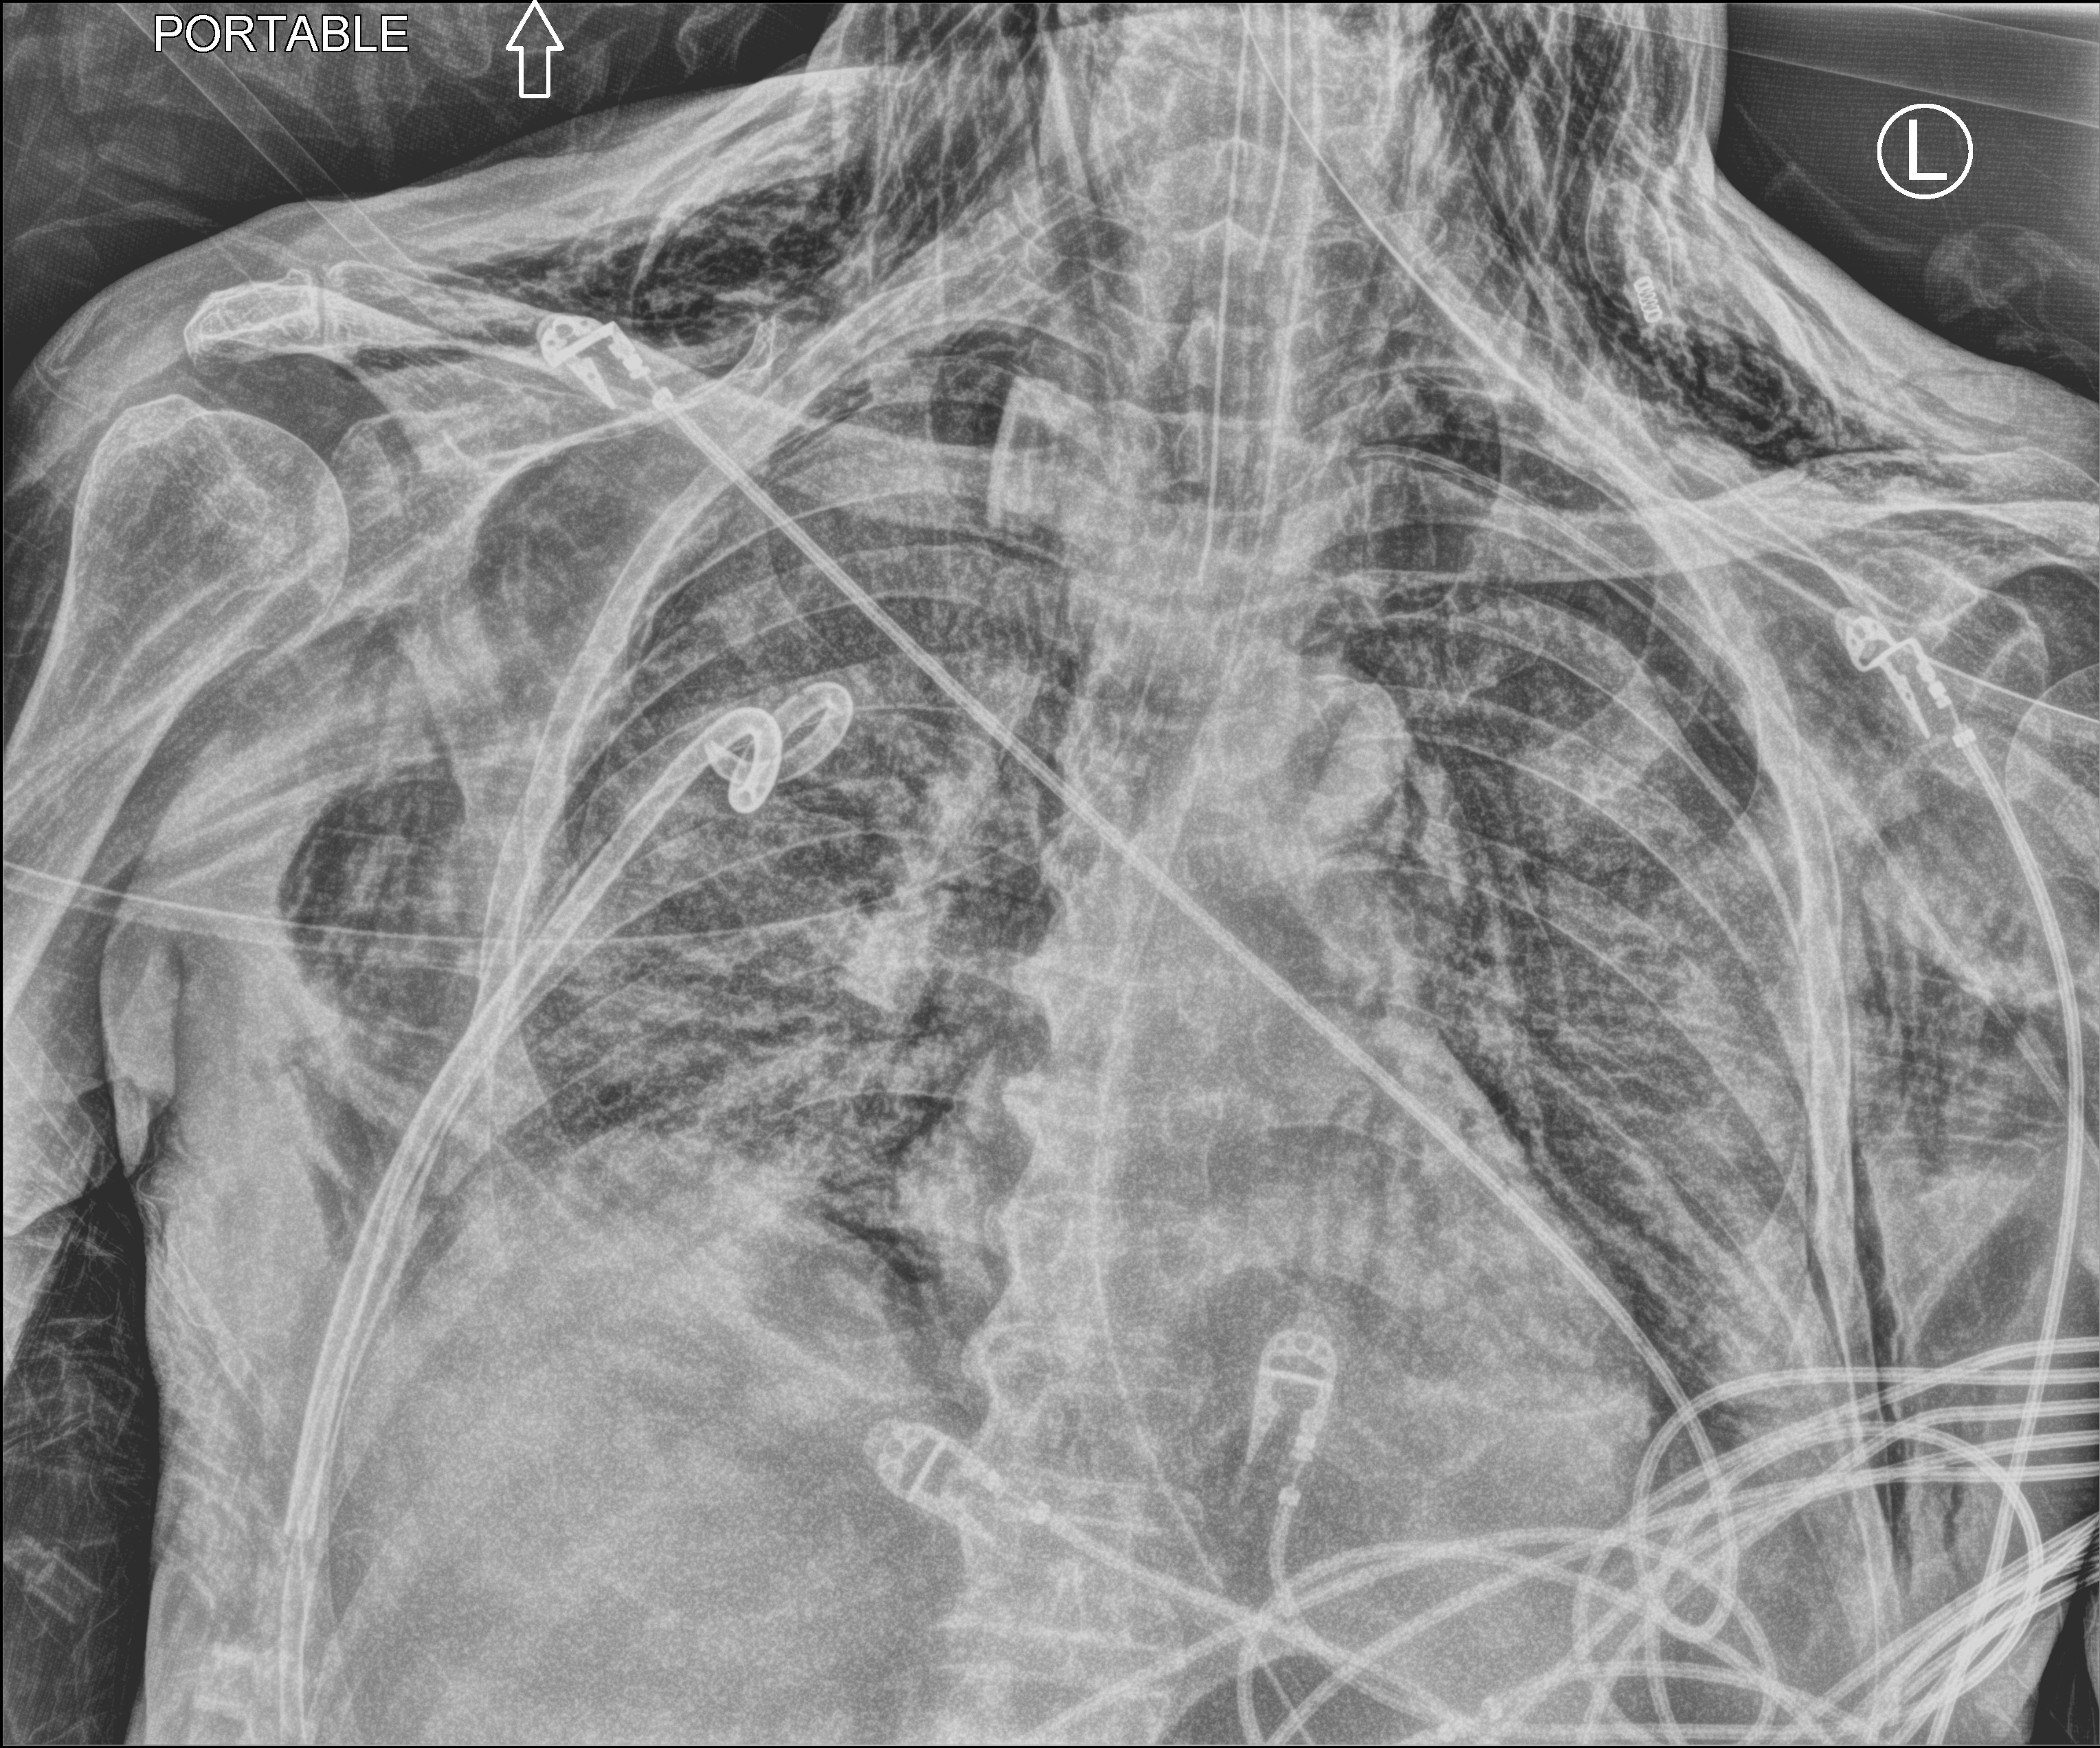
Chest X-ray (portable); anteroposterior (AP) projection. Male patient hospitalised with COVID-19, age 75–90 years.
From the hospital-stay record, not from the radiograph (when in the stay this image was taken is not recorded):
- admitted to intensive care during this hospital stay: yes
- length of hospital stay: 30 days